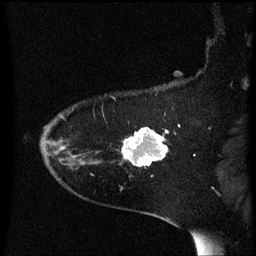
Breast MRI (dynamic contrast-enhanced), one sagittal slice; slice 46 of 60 in the series (ordered by position); dynamic contrast-enhanced series, image 2 of 3 at this slice position (ordered by acquisition); 1.5 T; TE 4.2 ms, TR 8.4 ms; 2 mm slice thickness; 256 × 256 image matrix, field of view 200 × 200 mm. Female patient, age 54 years. From the clinical record (not read from this slice): setting: breast cancer imaged before/during neoadjuvant chemotherapy; receptor status: HR-positive, HER2-negative.
Structures marked on this image (semi-automatic segmentation, software-assisted and operator-edited):
- analysis volume of interest (the breast-tissue region the enhancement analysis was run in; not a lesion): bounding box <123,128,169,167> (left, top, right, bottom; pixels)
- tumour enhancement mask (voxels above the 70 % enhancement threshold inside the analysis volume of interest): <123,128,169,167>